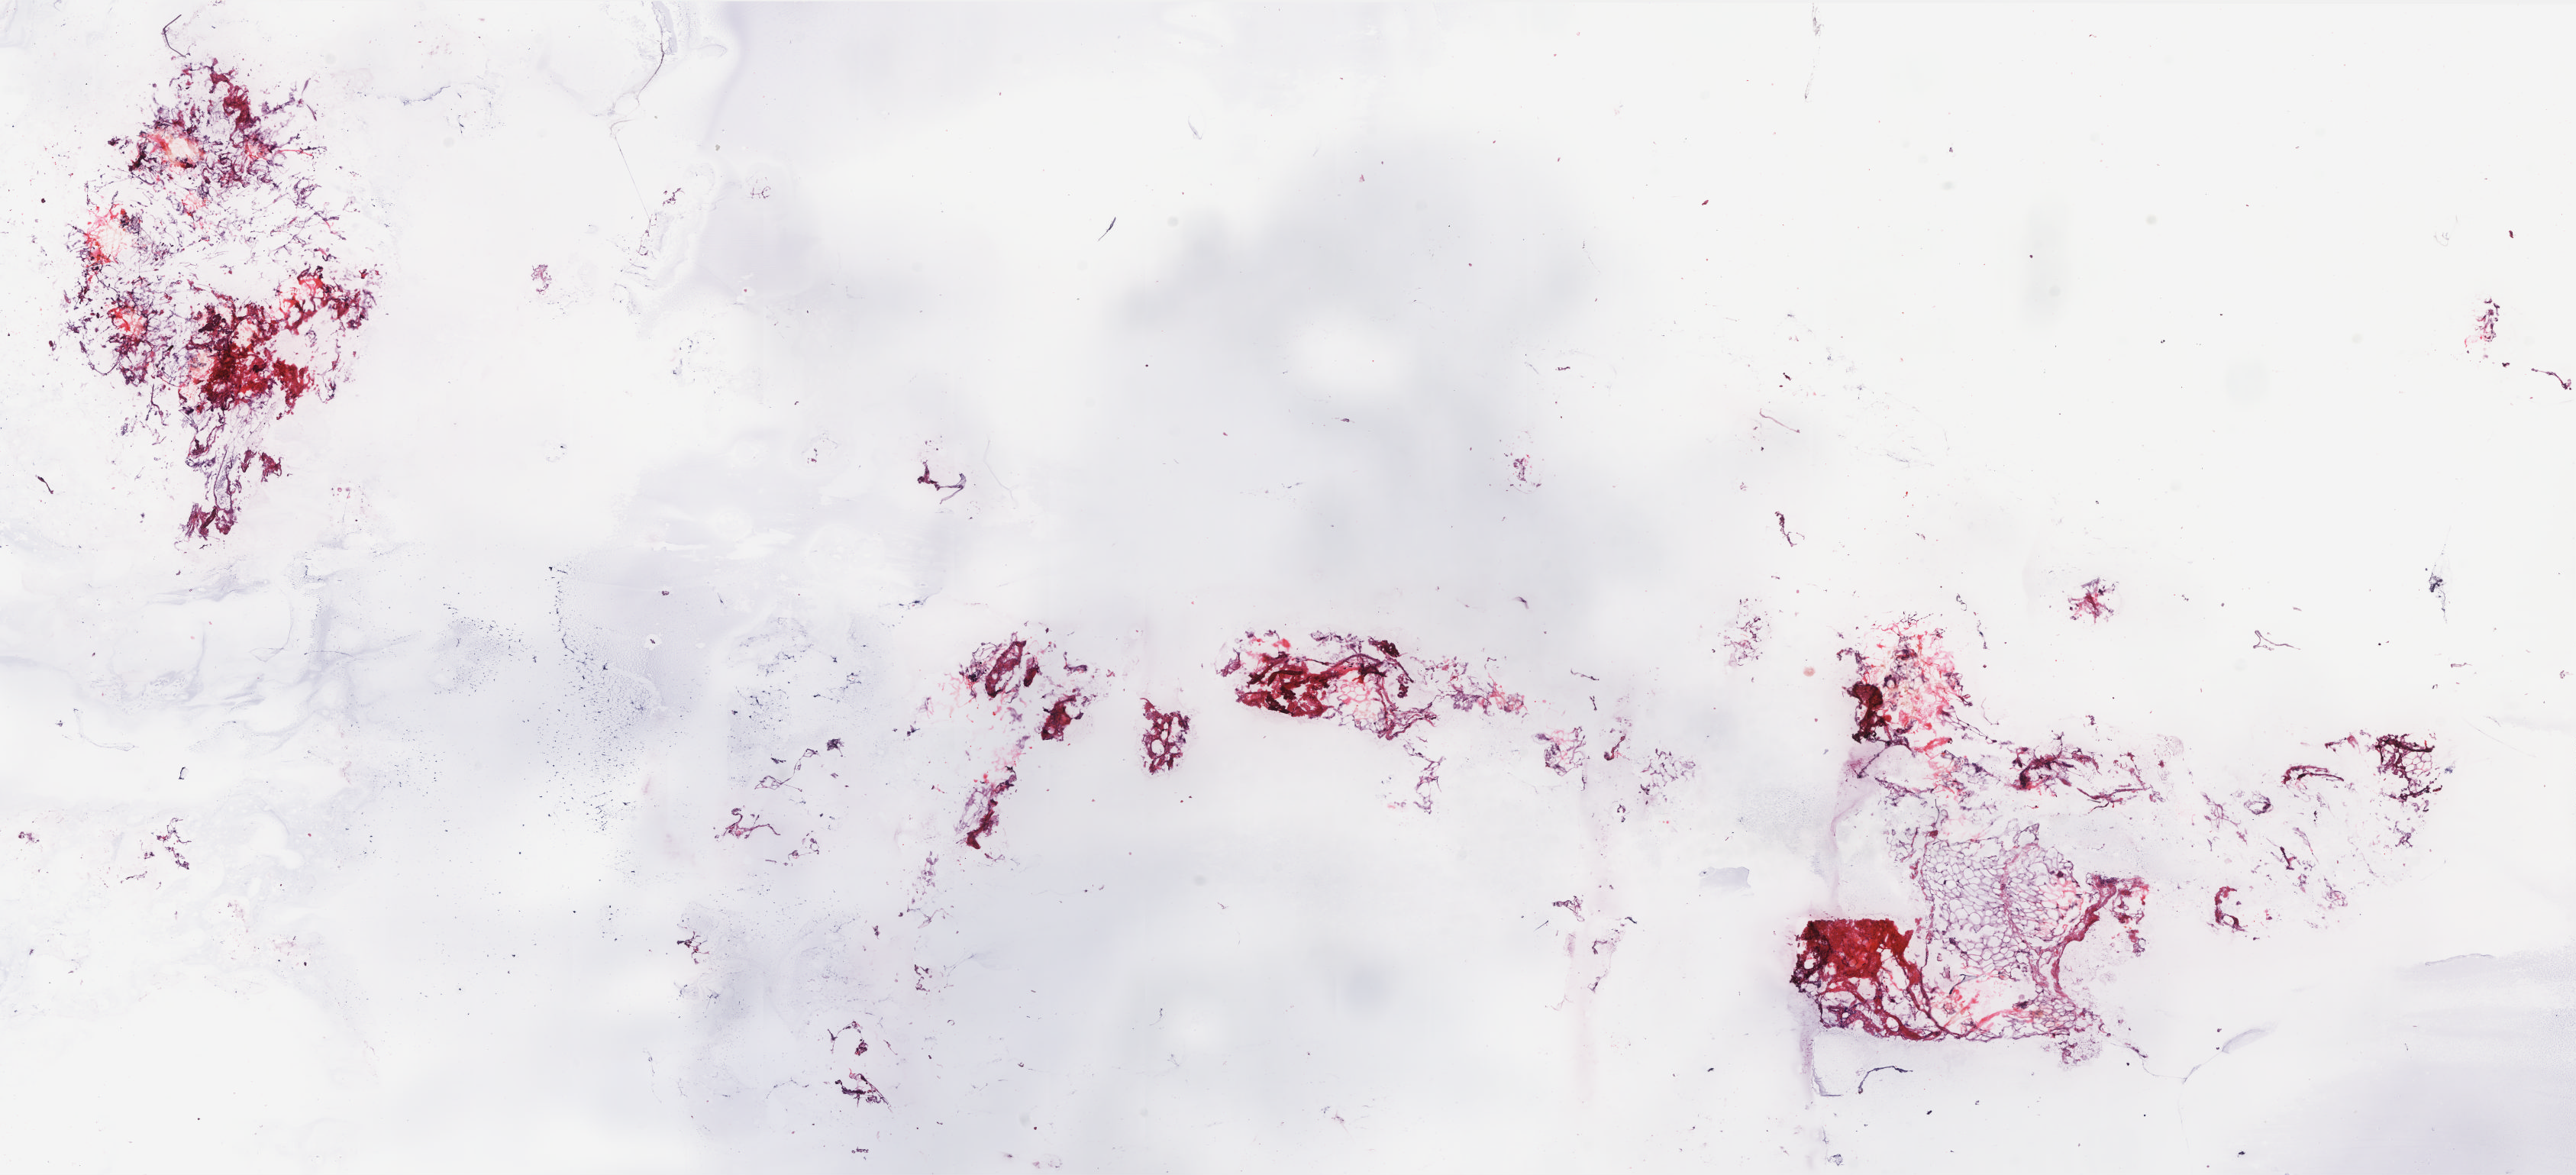
H&E-stained whole-slide image — a low-resolution overview of the entire scanned area, about 26.9 x 12.3 mm (from a 20x scan); frozen section from the top of the tissue portion; breast, solid tissue normal (non-tumour tissue) sample. Female, age 37 years at initial diagnosis. Slide review estimates, as recorded: tumour cells 0%, tumour nuclei 0%, normal cells 0%, stromal cells 100%, necrosis 0%. Inflammatory infiltration, as recorded: lymphocyte infiltration 1%, monocyte infiltration 5%, neutrophil infiltration 0%.
* this section: solid tissue normal sample (biorepository sample class)
* patient diagnosis: Infiltrating duct carcinoma, NOS